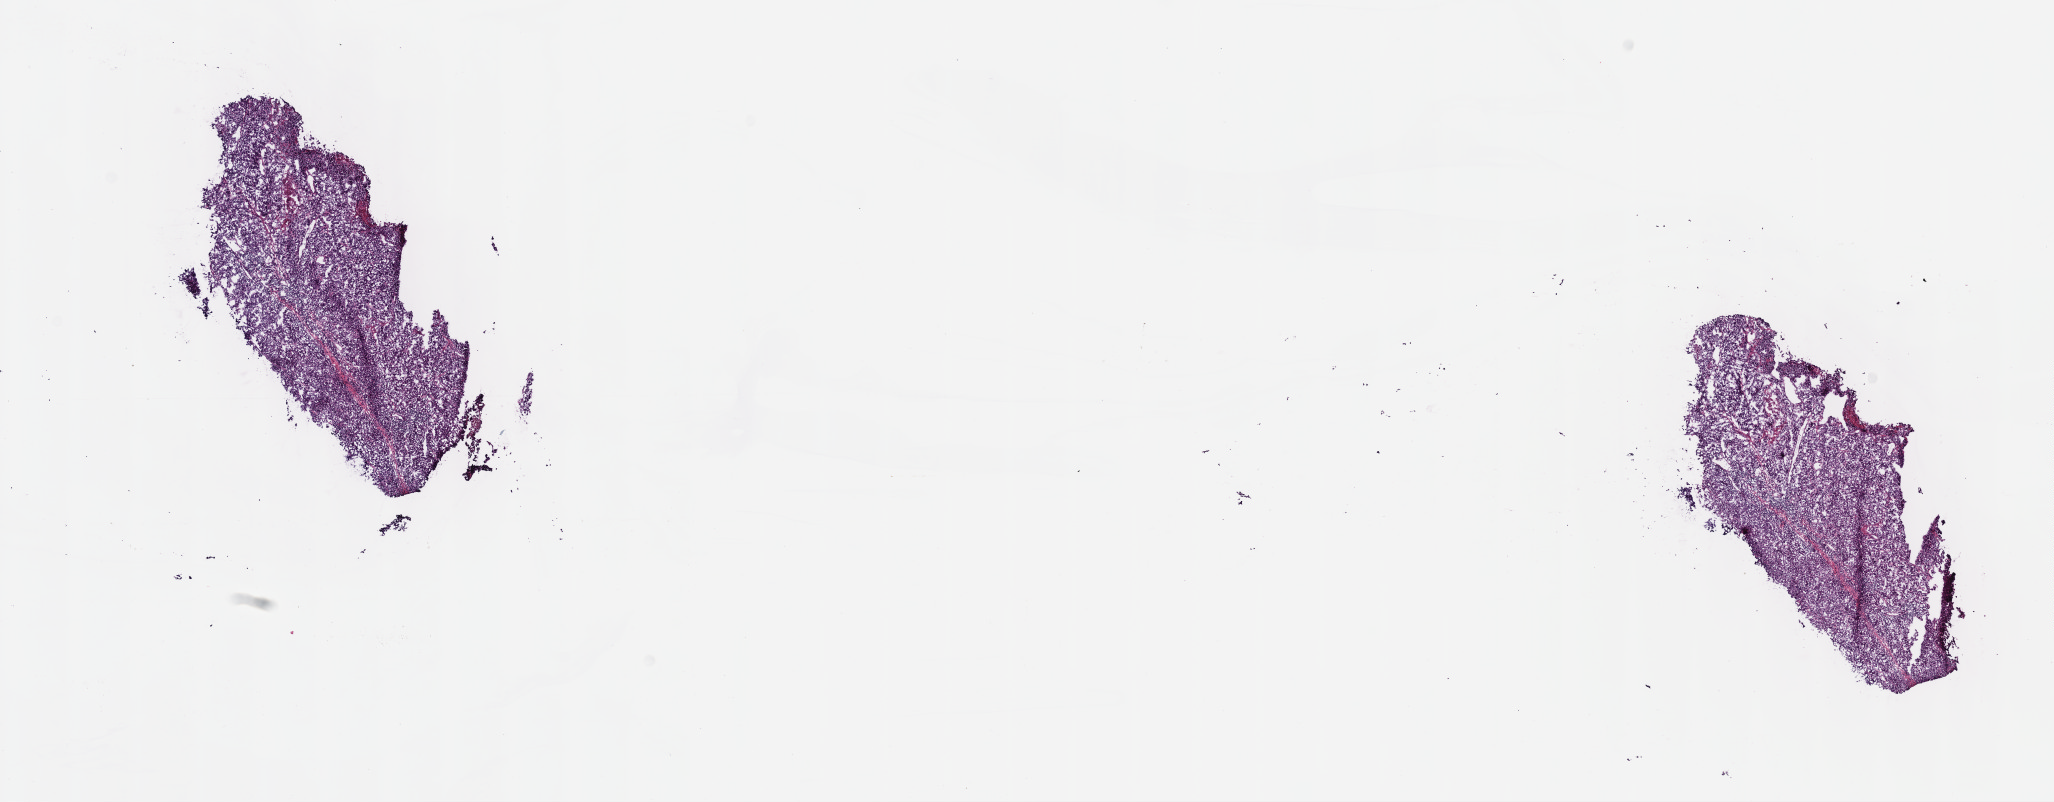
Whole-slide histology image, H&E — shown as a low-resolution overview of the whole scanned area (about 16.6 x 6.5 mm). Frozen section from the top of the tissue portion. Metastatic tumour sample. Male, age 63 years at initial diagnosis. Pathologist review of this section (percent, as recorded): tumour cells 97%, tumour nuclei 80%, normal cells 0%, stromal cells 0%, necrosis 3%. Infiltration values recorded for this section: lymphocyte infiltration 2%, monocyte infiltration 0%, neutrophil infiltration 0%.
• this section: metastatic tumour tissue
• patient diagnosis: Malignant melanoma, NOS